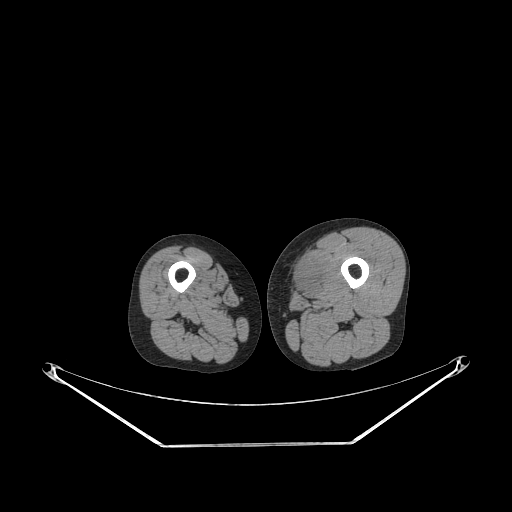
CT of an extremity soft-tissue mass (from a PET/CT study), one axial slice; slice 225 of 267 in the series (ordered by position); reconstruction kernel STANDARD; 140 kVp; soft-tissue window (W 400 / L 40 HU); 3.75 mm slice thickness; 512 × 512 image matrix, field of view 500 × 500 mm. Male patient. Case-level facts recorded for this patient, not image findings: histological type: pleiomorphic leiomyosarcoma; grade: high; site of the primary tumour: left thigh.
Annotated regions visible in this slice (expert contour drawn on MRI and transferred to this co-registered scan by the dataset authors):
- gross tumour volume including surrounding oedema: bounding box (x1, y1, x2, y2) in pixels: (288, 251, 328, 295)
- gross tumour volume (mass): (290, 256, 321, 293)